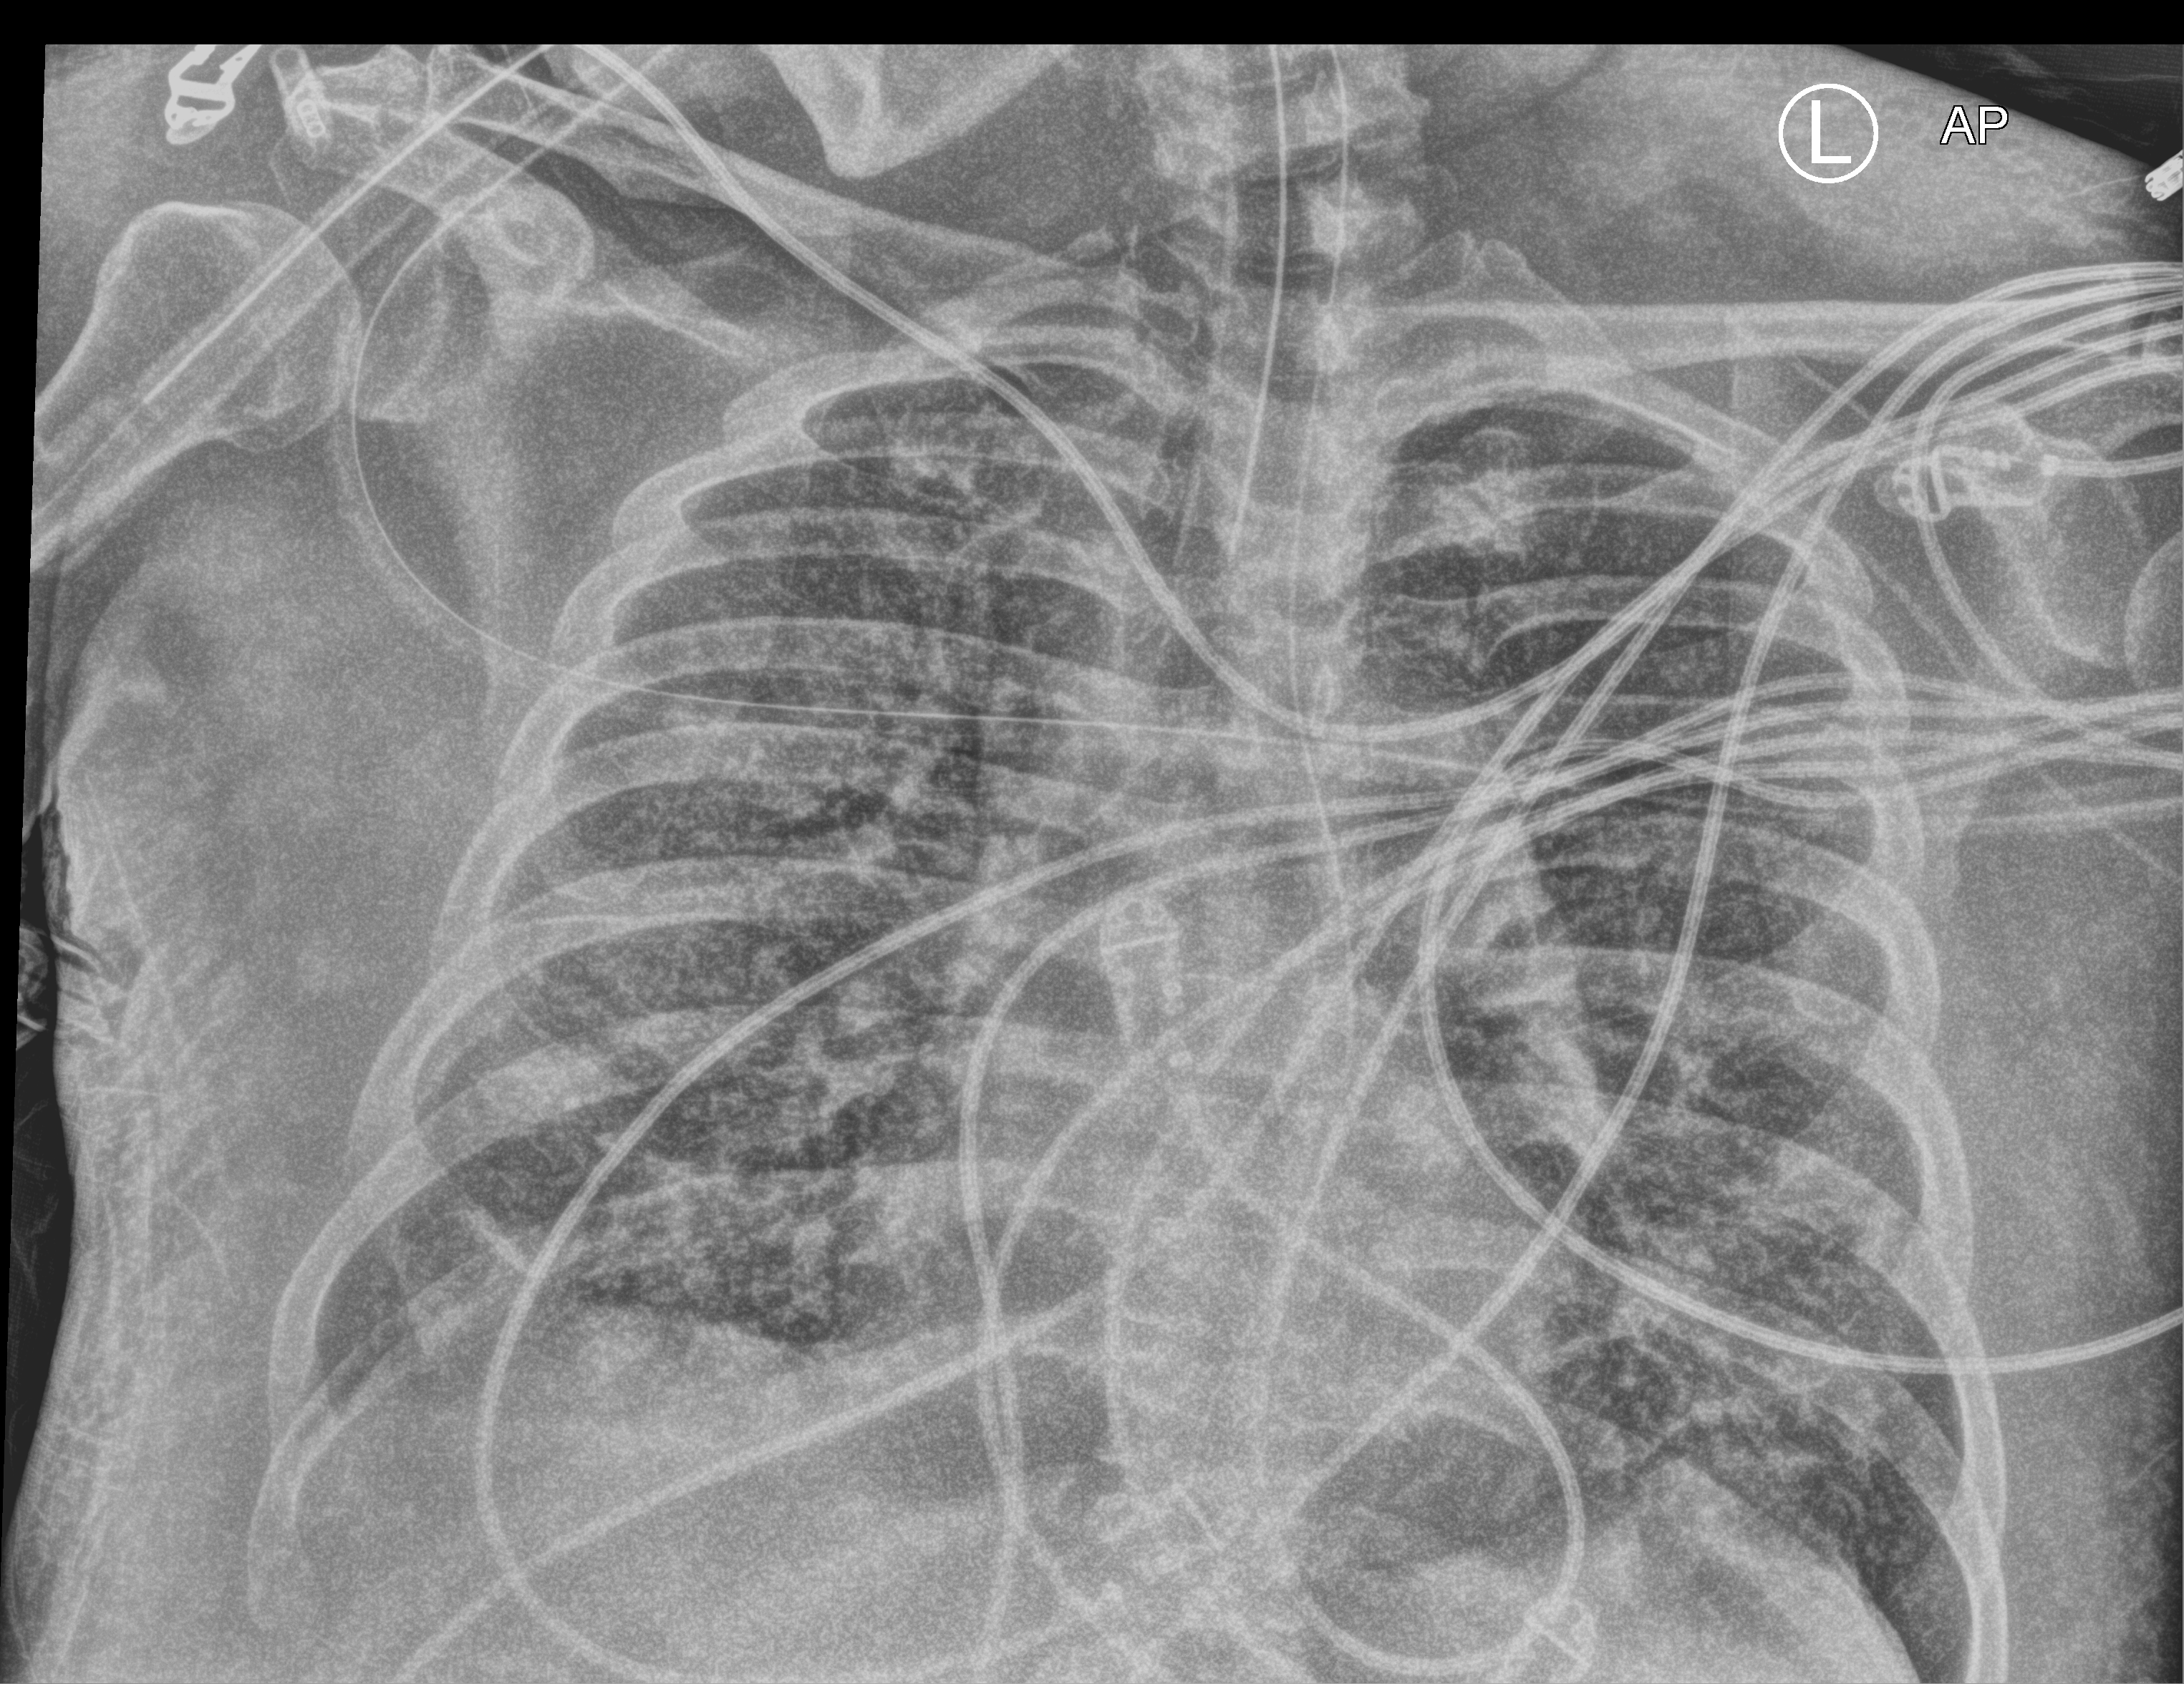
Chest X-ray (portable), anteroposterior (AP) projection. Male patient hospitalised with COVID-19, age 60–74 years.
From the hospital-stay record, not from the radiograph (when in the stay this image was taken is not recorded): mechanically ventilated during this hospital stay: yes; admitted to intensive care during this hospital stay: yes; diabetes (admission record): no.